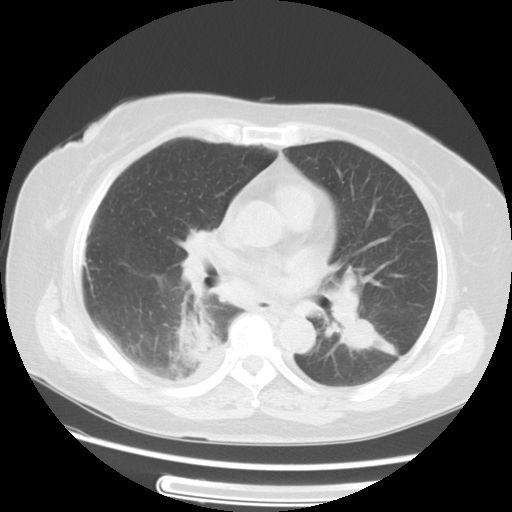
Chest CT, one axial slice; position 32 of 57 along the scan axis; reconstruction kernel STANDARD; 120 kVp; lung window (W 1500 / L -600 HU); 5 mm slice thickness; 512 × 512 image matrix. Patient: female, 69 years. From the clinical record (not read from this slice): clinical TNM (as recorded): T2 N1 M1a.
Annotated regions visible in this slice (bounding box drawn by a radiologist):
- lung tumour (recorded histology: adenocarcinoma): bounding box (x1, y1, x2, y2) in pixels: (175, 309, 214, 366)